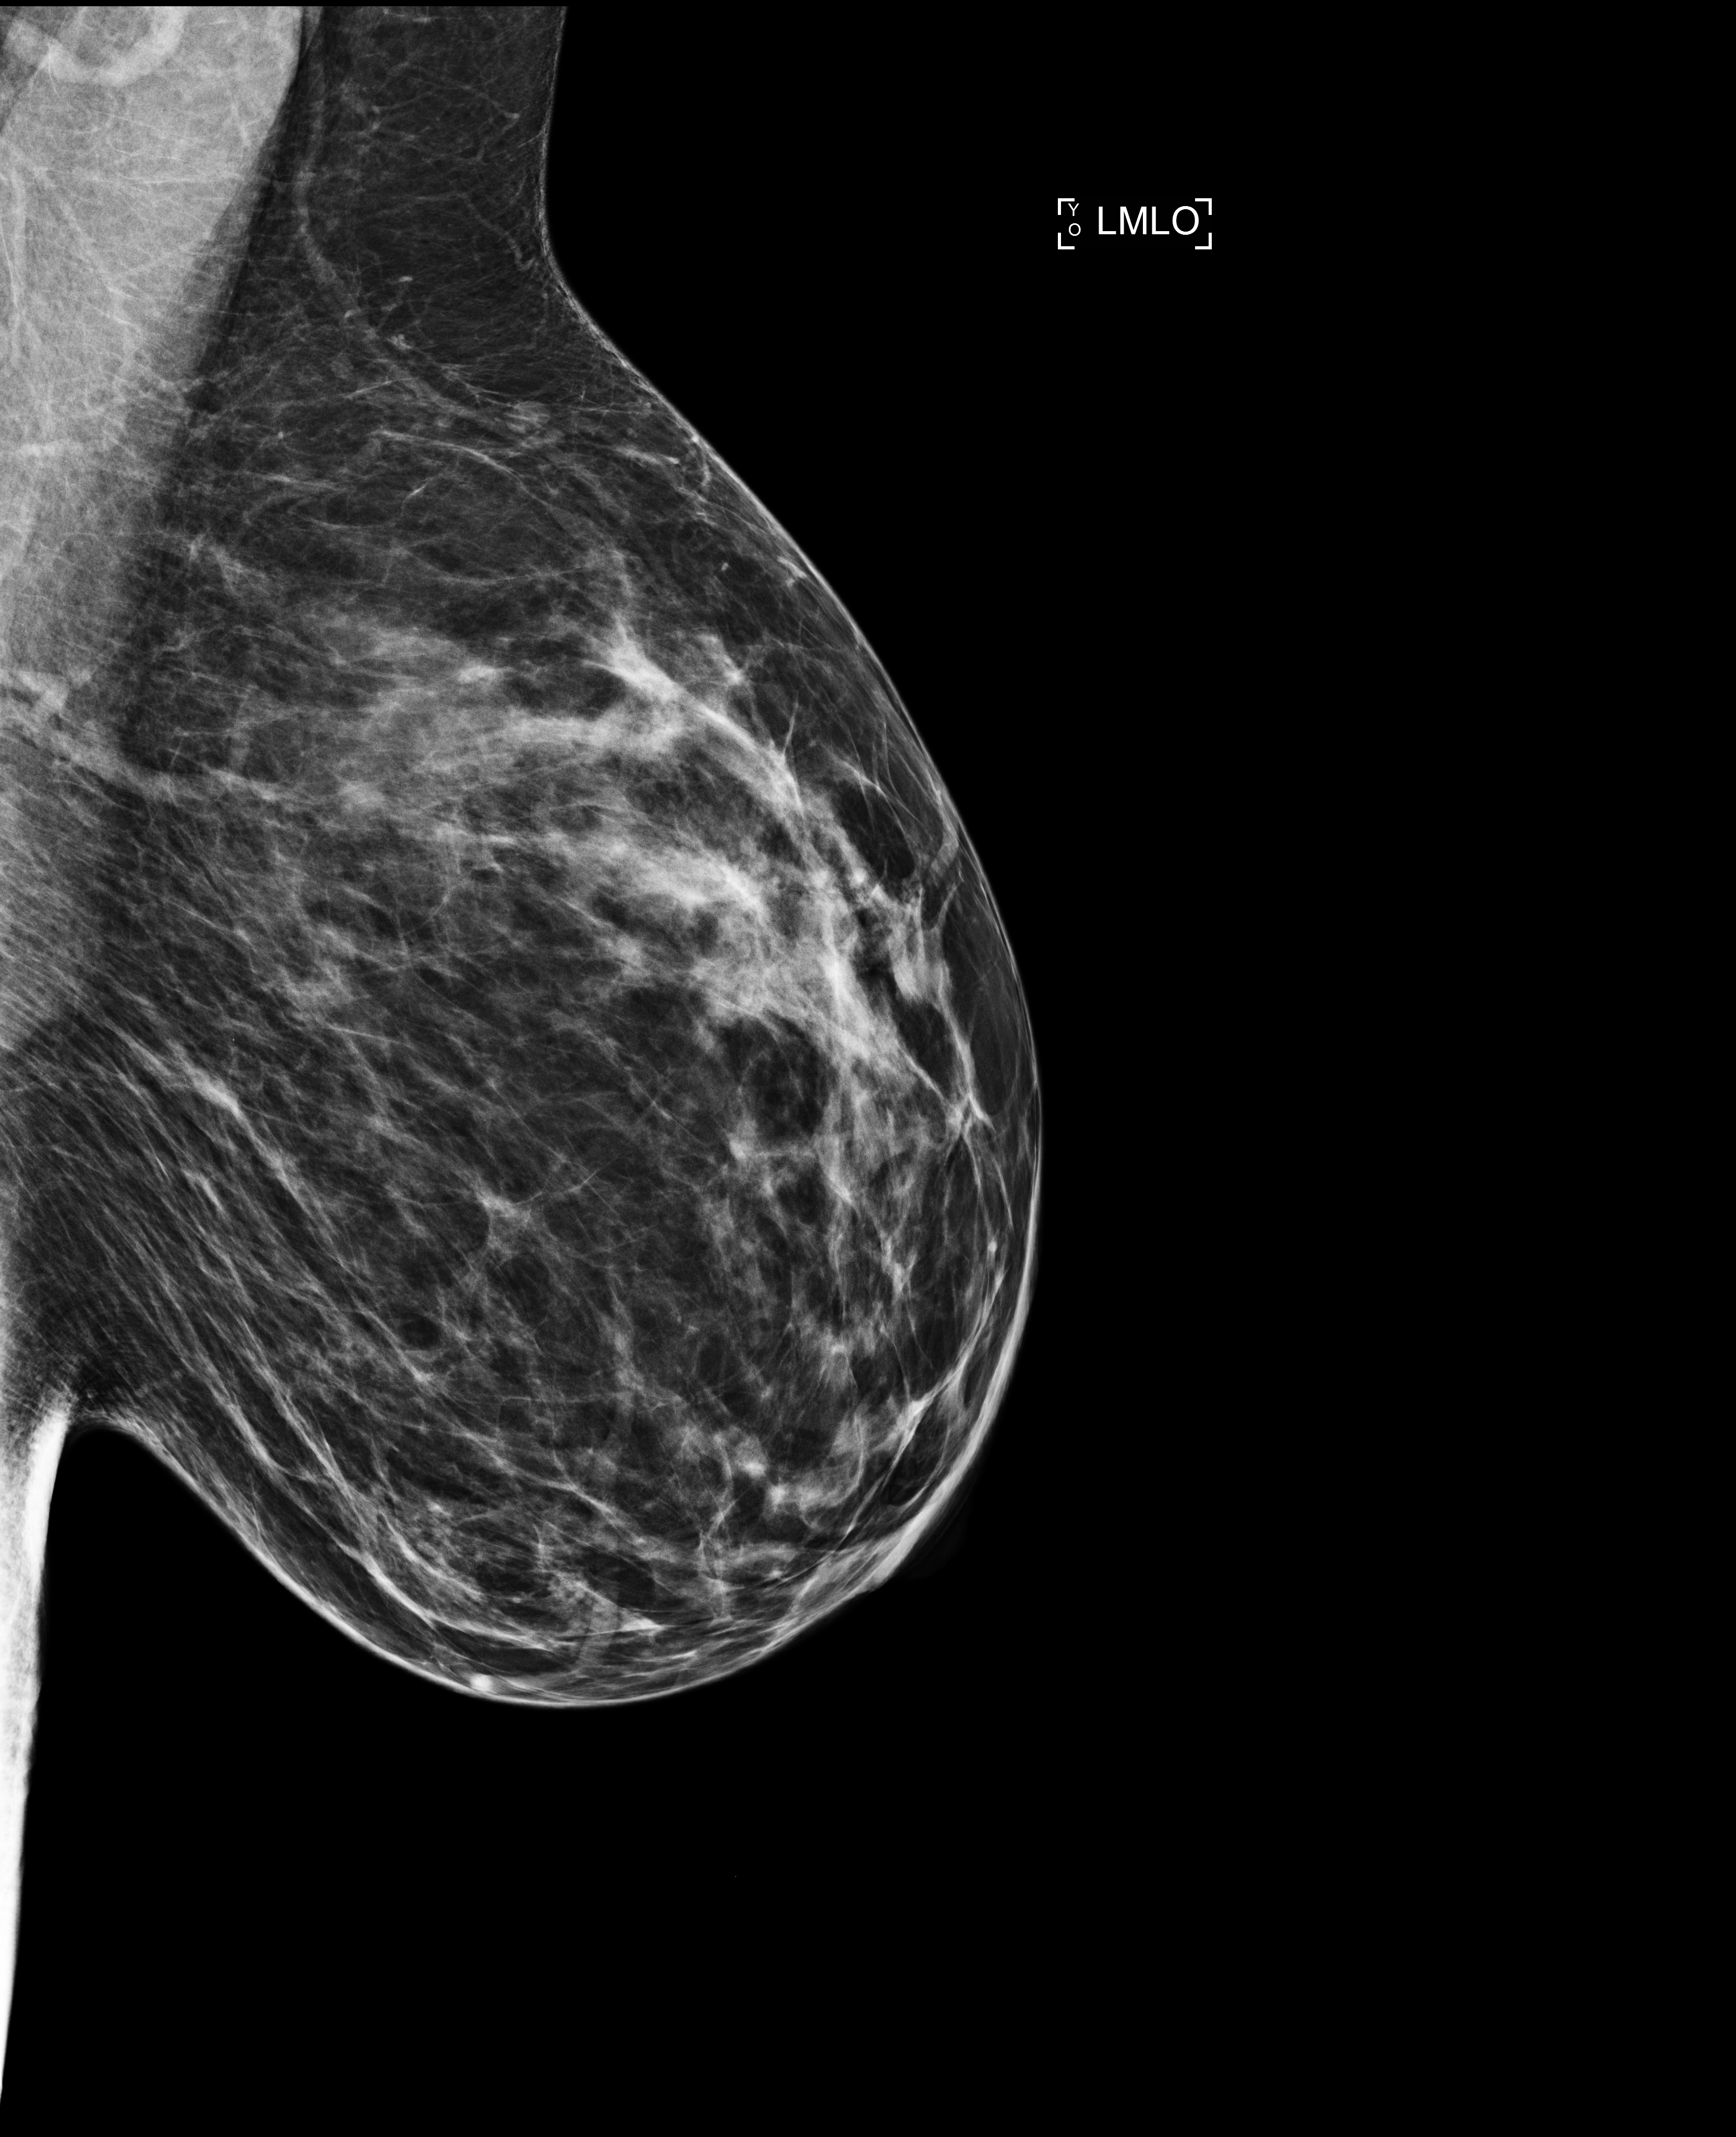
Annual screening mammography examination, compressed breast thickness 74 mm, system: Selenia Dimensions. Patient: female, 43 years.
Image type: full-field digital mammogram. Breast: left. Projection: medio-lateral oblique projection.